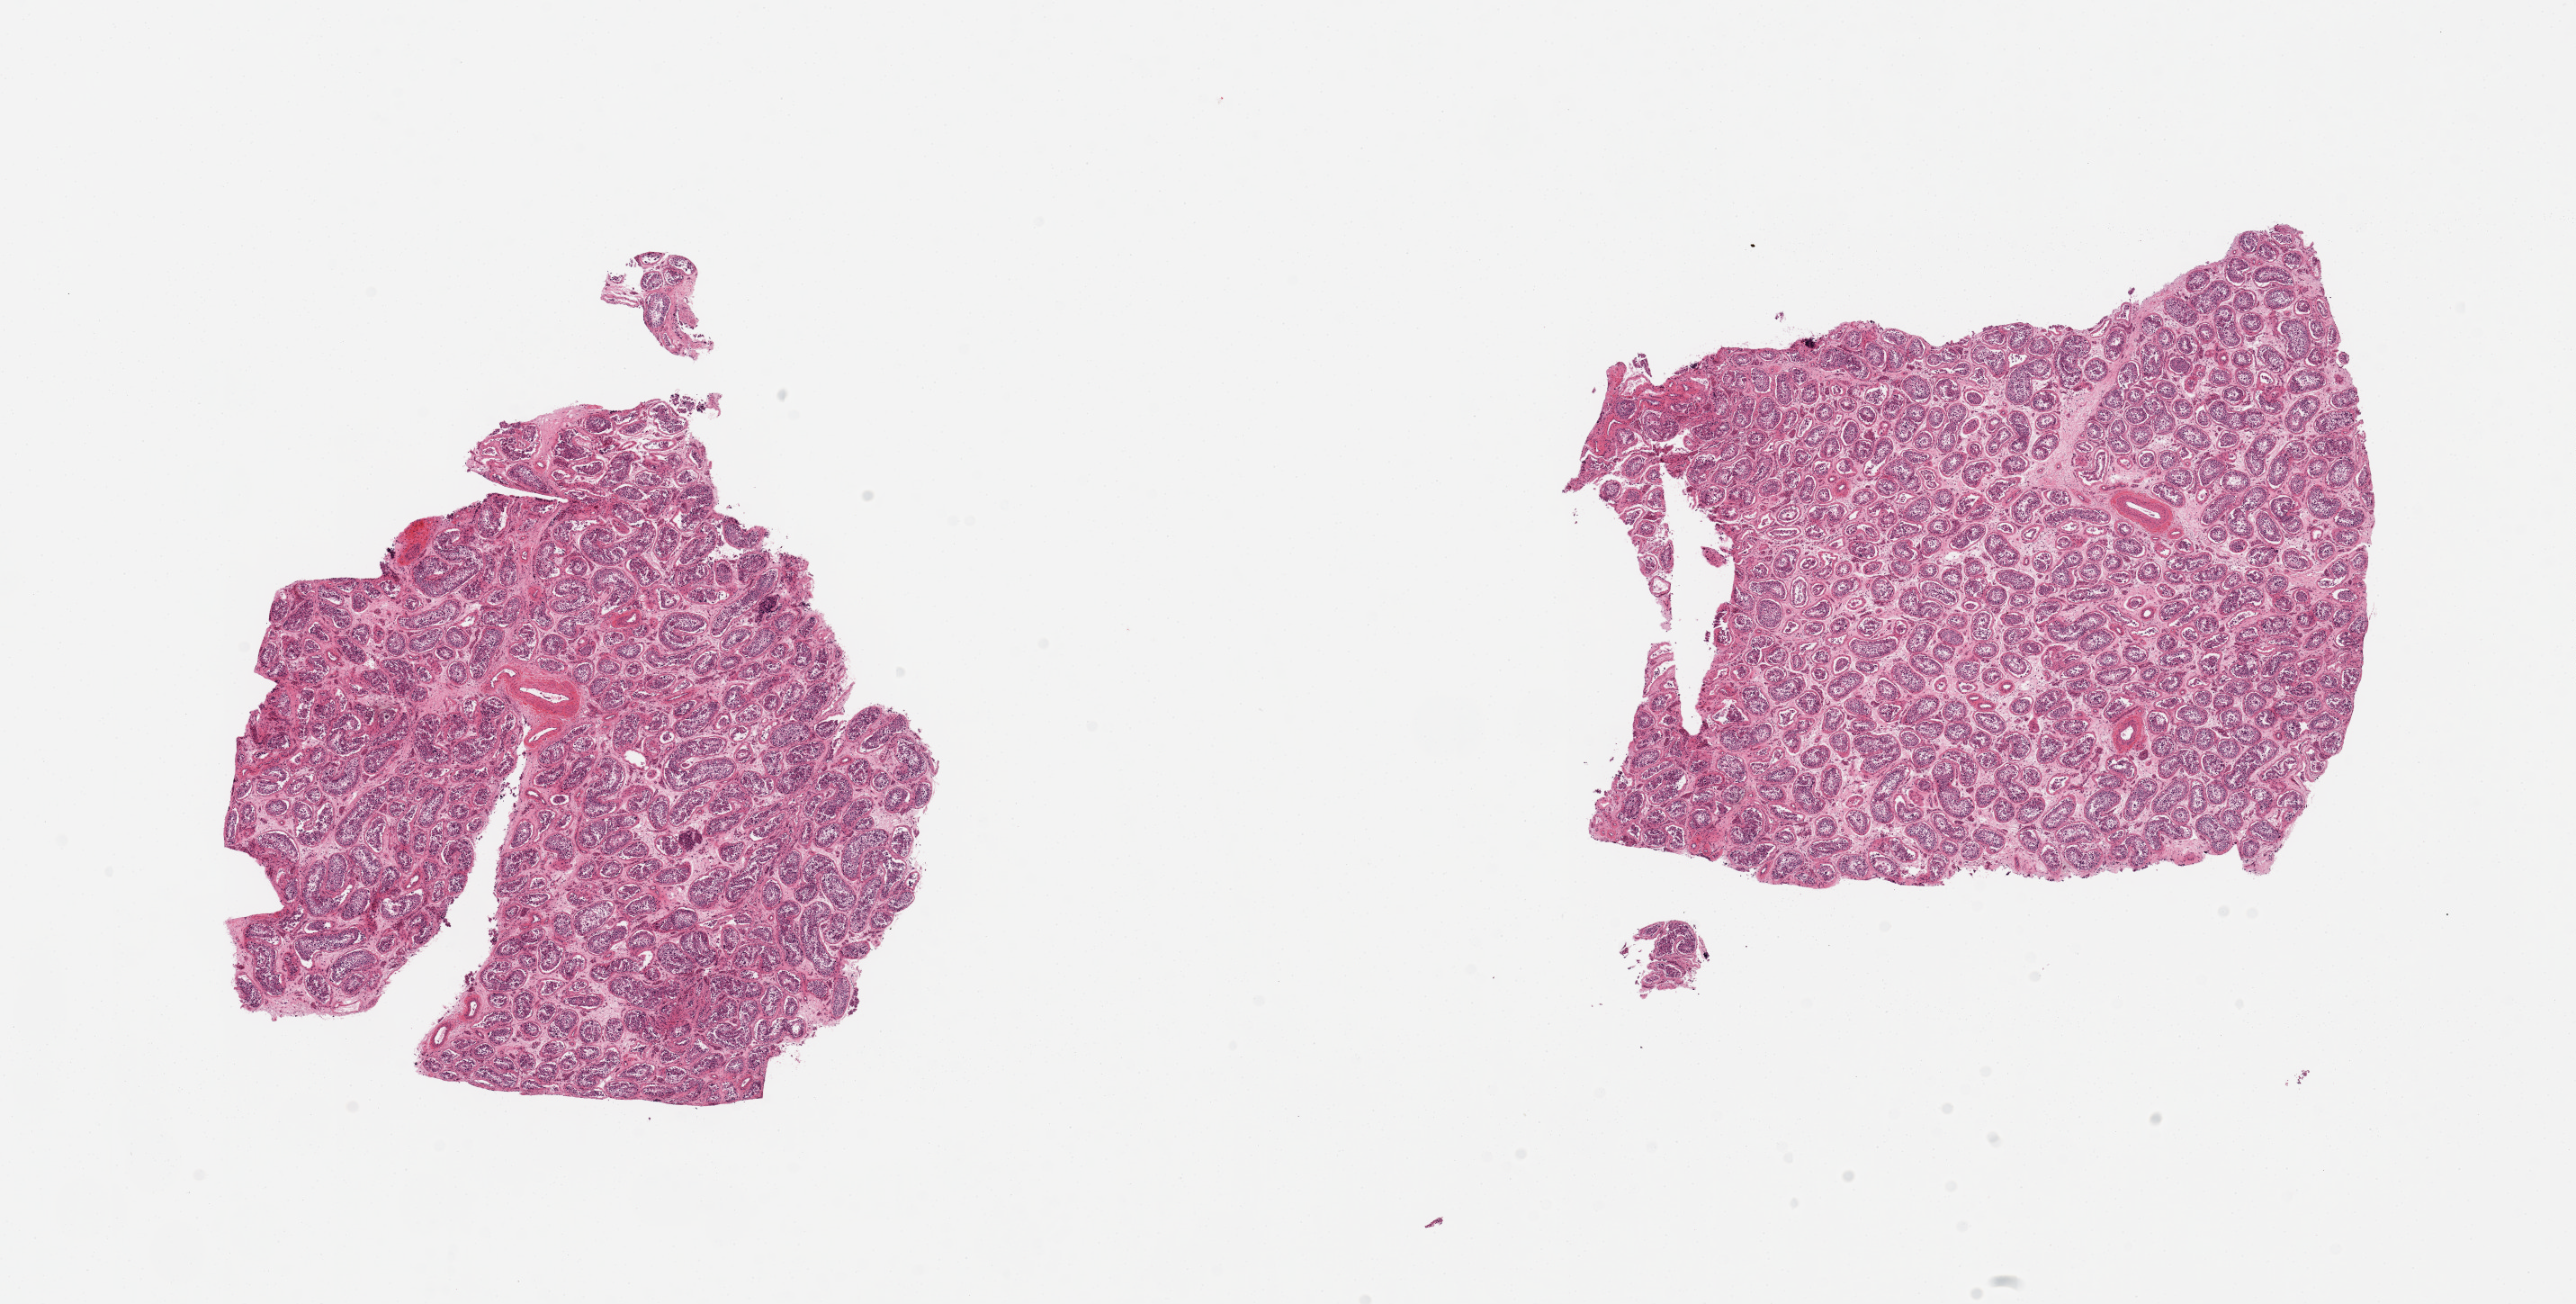
Whole-slide image, H&E stain, shown as a low-resolution overview of the whole scanned area (about 22.6 x 11.5 mm, slide scanned at 20x); PAXgene-fixed, paraffin-embedded tissue; sampled site (target tissue): testis; tissue donor sample. Male donor.
Review note (as recorded): 2 pieces; spermatogenesis present.